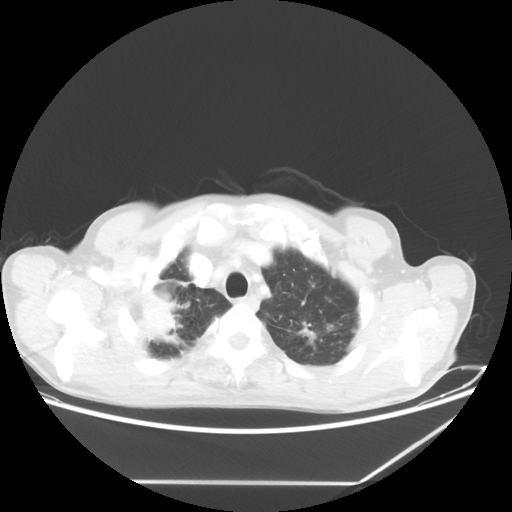
Chest CT, one axial slice; slice 56 of 65 in the series (ordered by position); 80 kVp; lung window (W 1500 / L -600 HU); 512 × 512 image matrix, field of view 397 × 397 mm. Patient: male, 68 years. From the clinical record (not read from this slice): clinical TNM (as recorded): T3 N3 M0.
Outlined on this slice (bounding box drawn by a radiologist):
- lung tumour (recorded histology: adenocarcinoma): bounding box (x1, y1, x2, y2) in pixels: (129, 279, 193, 348)